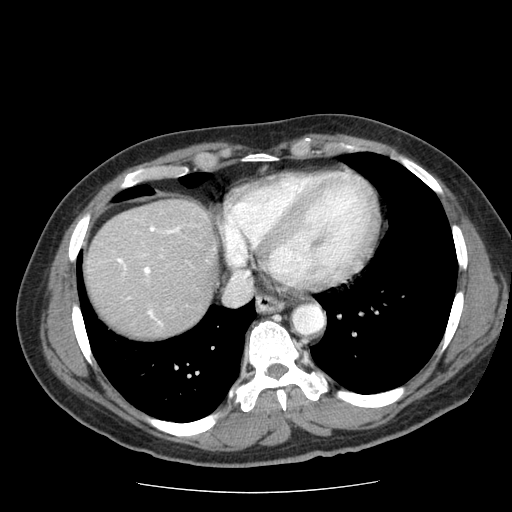
Contrast-enhanced abdominal CT (liver protocol), one axial slice; position 65 of 85 along the scan axis; reconstruction kernel STANDARD; soft-tissue window (W 400 / L 40 HU); 2.5 mm slice thickness; 512 × 512 image matrix. Case-level facts recorded for this patient, not image findings: diagnosis: hepatocellular carcinoma (patient treated with transarterial chemoembolisation; whether this scan precedes or follows treatment is not stated here); TNM stage (as recorded): Stage-IIIA.
Outlined on this slice (semi-automatic segmentation, software-assisted and operator-edited):
- liver parenchyma outside the tumour (the mass and vessels are separate outlines, so this box may not span the whole liver): box from (x=84, y=198) to (x=217, y=338) px
- liver vessels: (x=117, y=226)–(x=180, y=326)